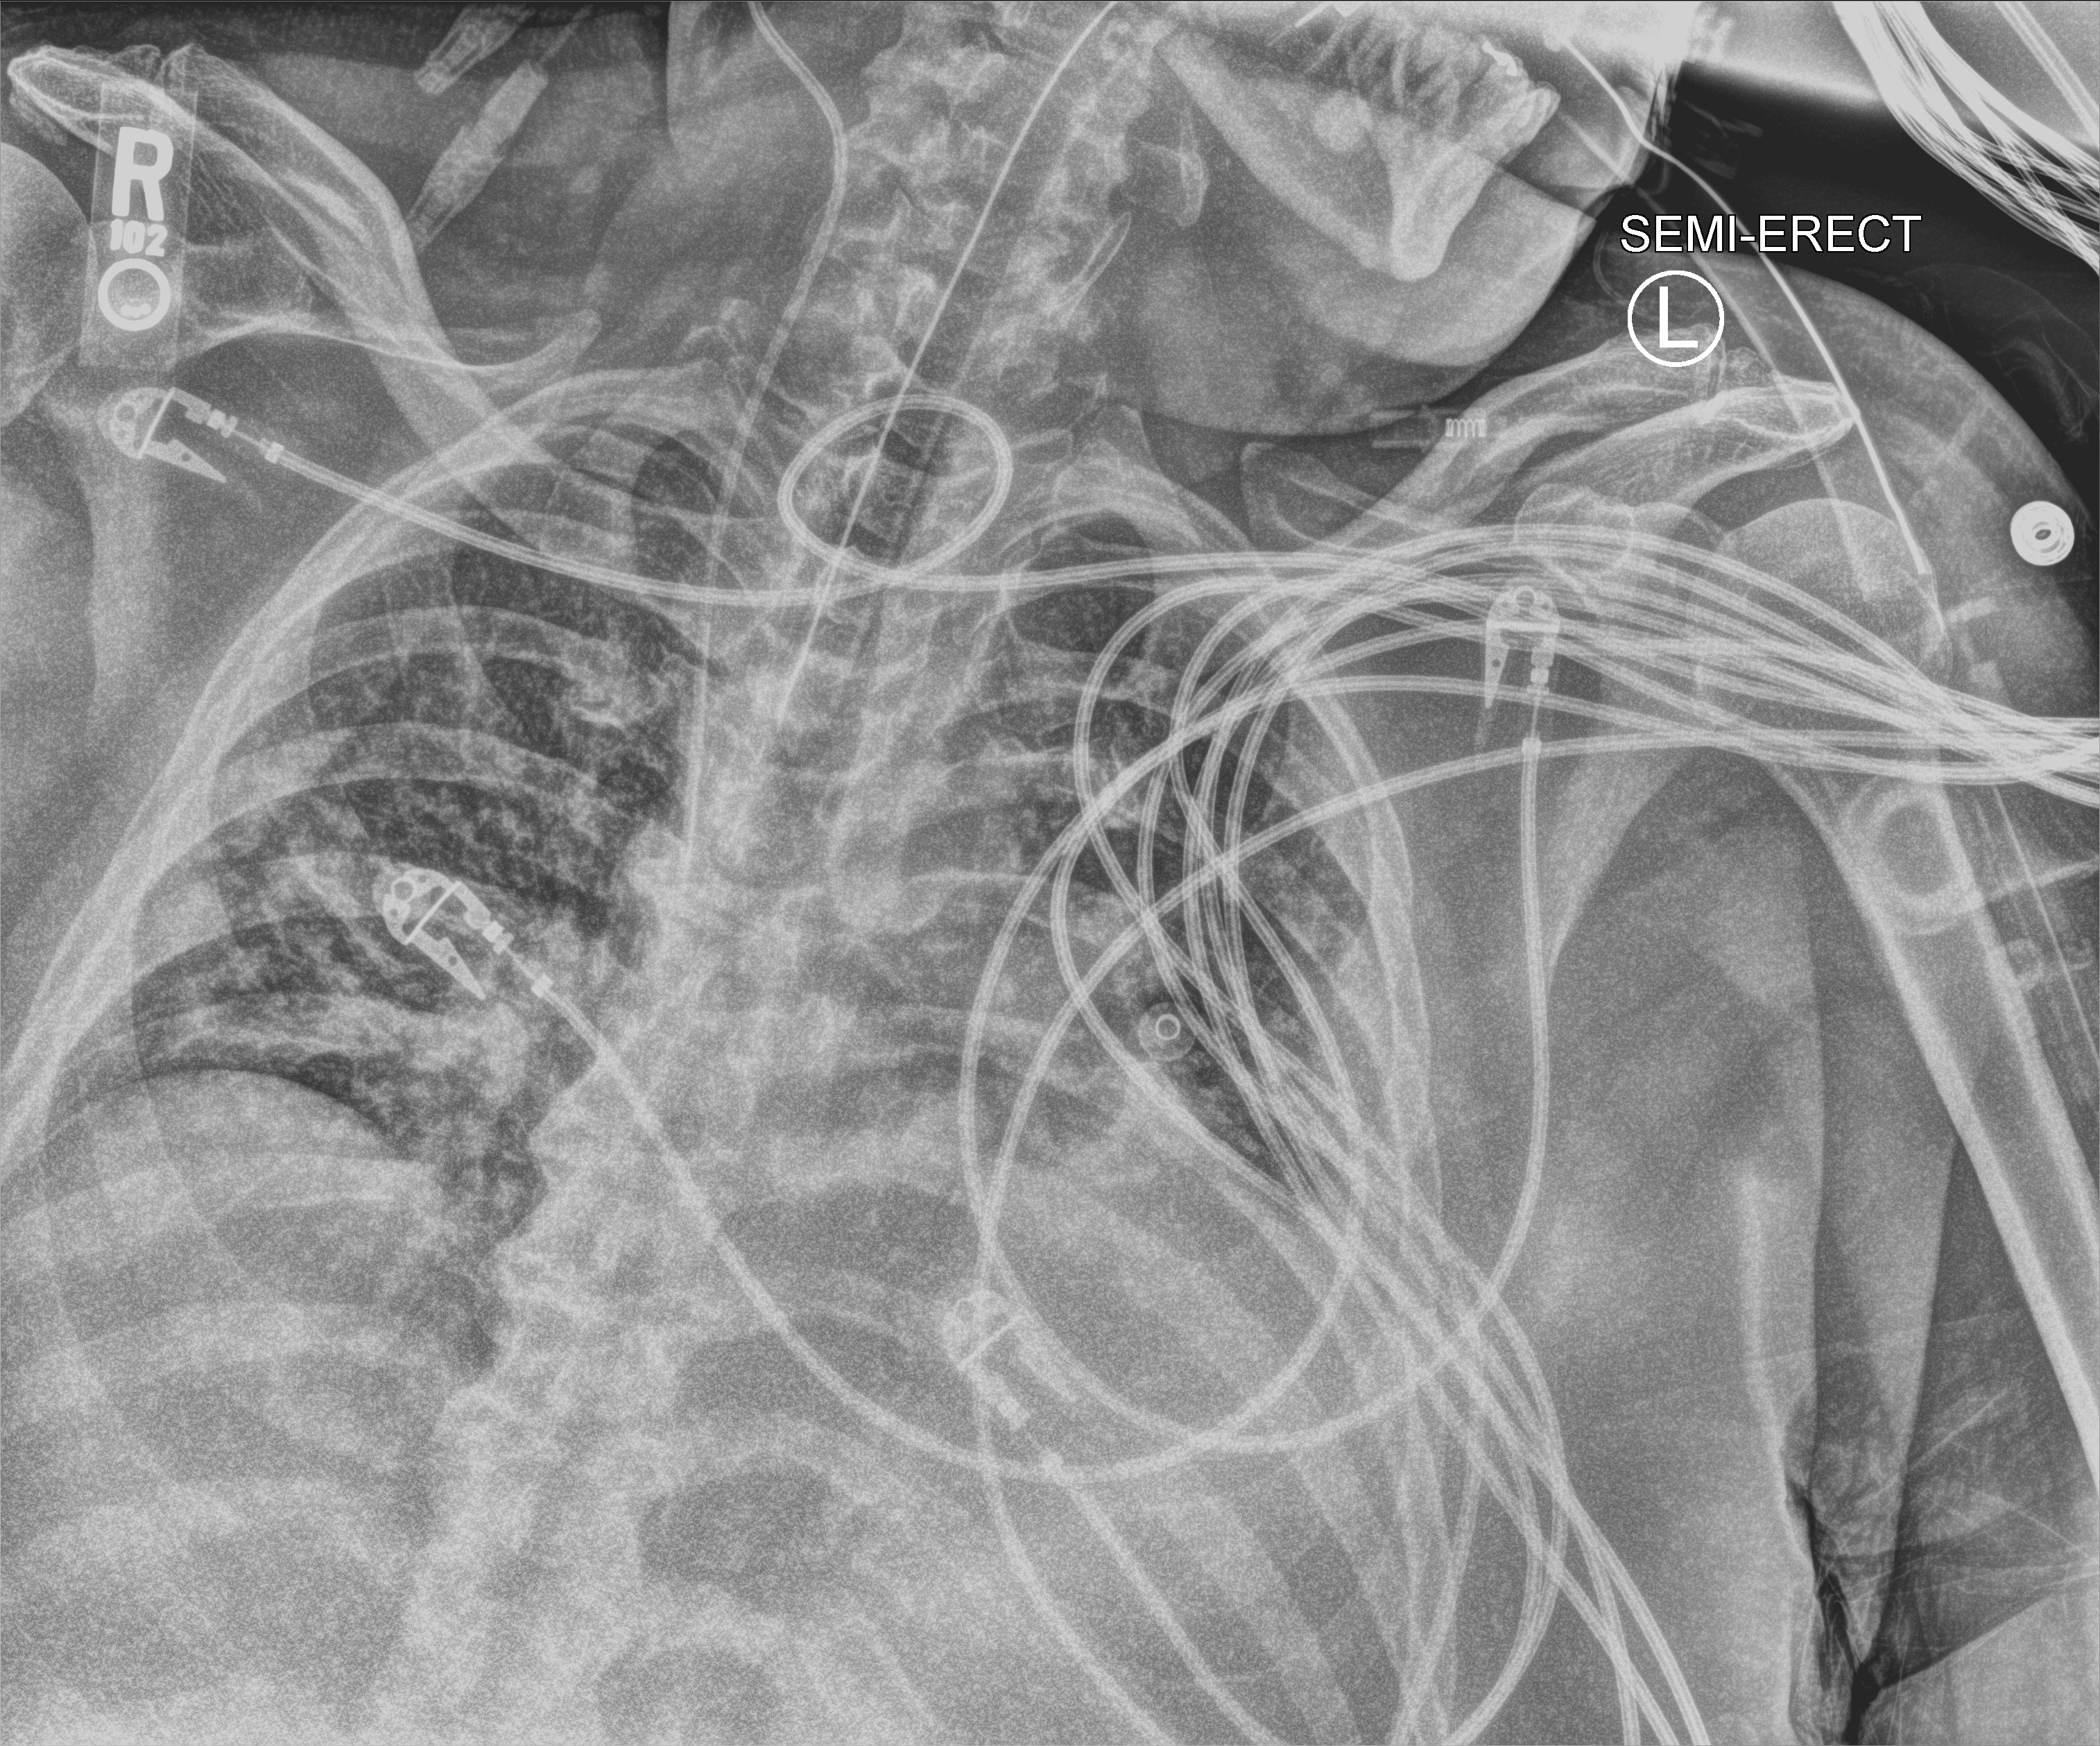
Chest X-ray (portable). Male patient hospitalised with COVID-19, age 18–59 years.
Hospital-stay facts (about this admission, not read from this image; timing relative to this image not recorded): admitted to intensive care during this hospital stay: yes; mechanically ventilated during this hospital stay: yes.